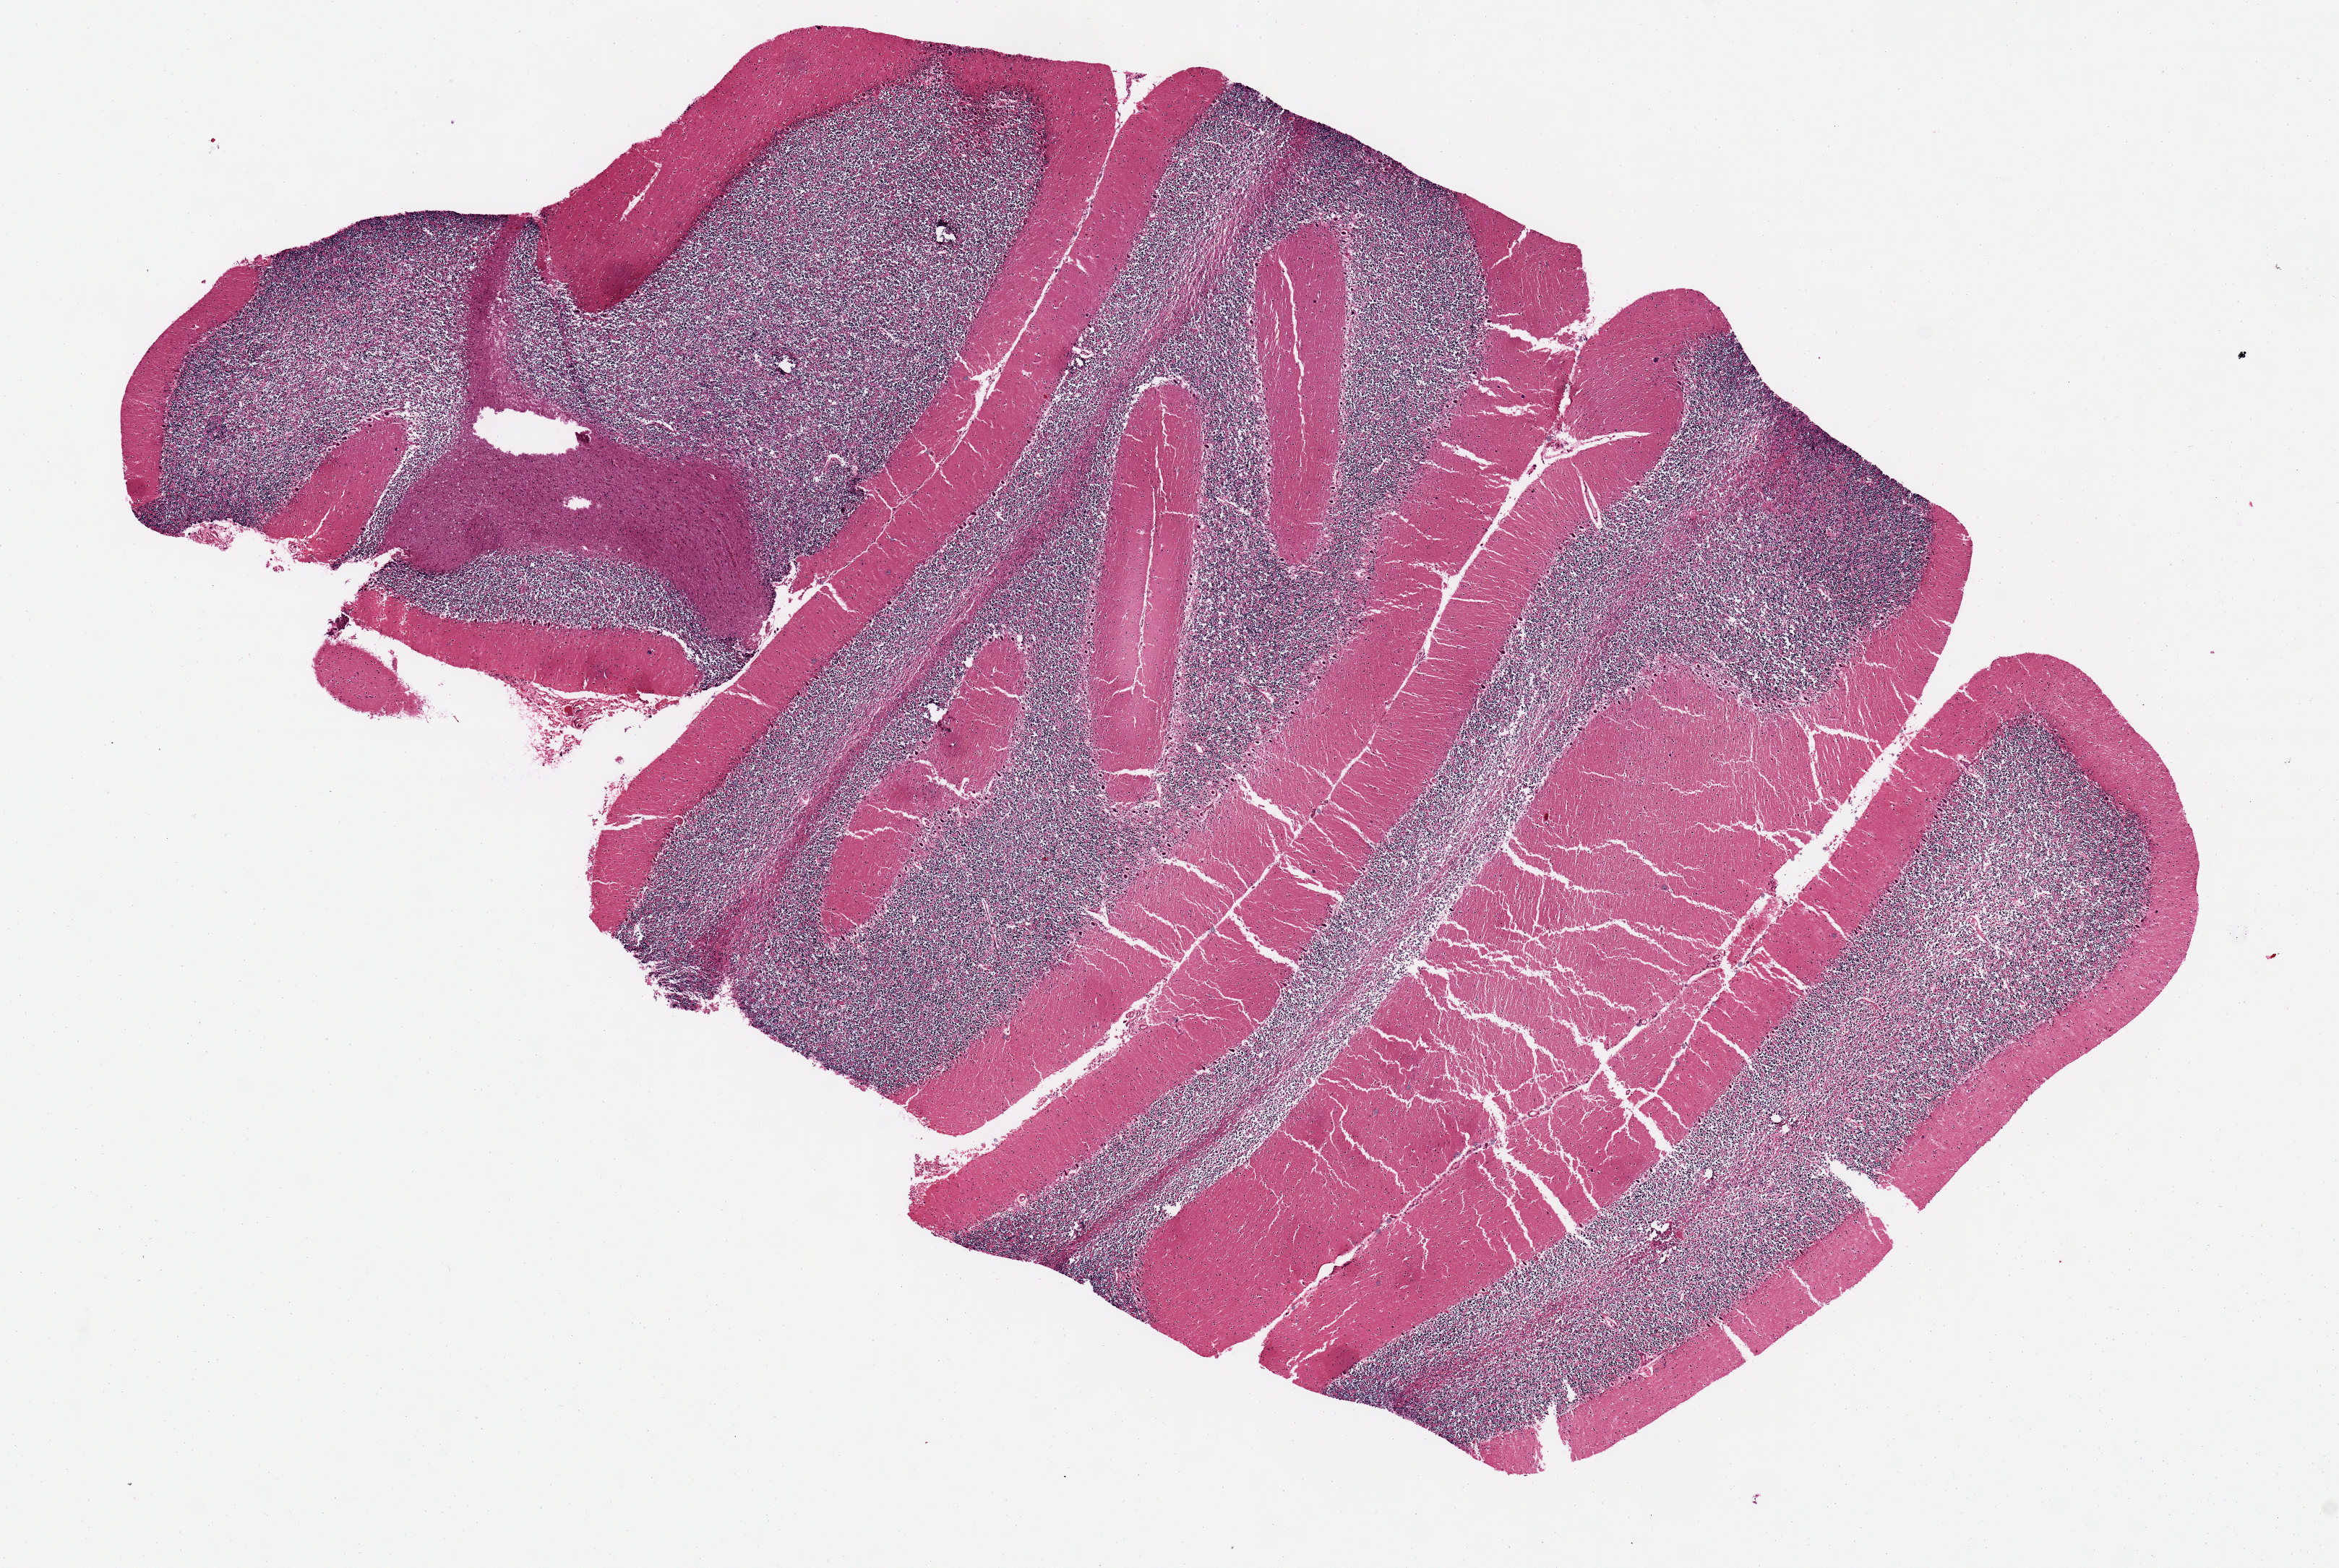
Whole-slide image, haematoxylin and eosin stain, low-resolution overview of the scanned area, about 12.8 x 8.6 mm (from a 20x scan), PAXgene-fixed, paraffin-embedded tissue, section of cerebellum (target tissue), donor tissue sample. Donor sex: female.
* review note (as recorded): Granular layer appears slightly autolyzed; outer layer many cracks (artifacts); last tissue fixed